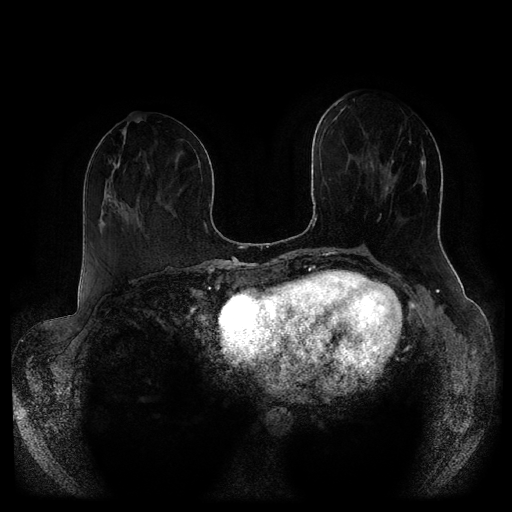
Breast MRI (dynamic contrast-enhanced, multi-phase), one axial slice. Slice 38 of 116 in the series (ordered by position). Dynamic contrast-enhanced series, time point 2 of 5 at this slice position (early post-contrast). 1.5 T. TE 2.6 ms, TR 5.3 ms. 512 × 512 image matrix, field of view 370 × 370 mm. Patient: female, 51 years.
Outlined on this slice (semi-automatically segmented with operator editing):
- breast lesion (labelled 'tumour' in the annotation; benign lesions carry a separate 'benign' label): bounding box <371,159,394,174> (left, top, right, bottom; pixels)